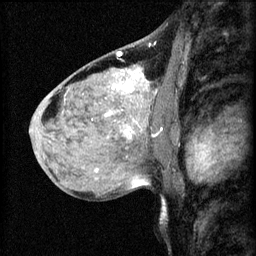
Breast MRI (dynamic contrast-enhanced), one sagittal slice; position 40 of 60 along the scan axis; 3 images stored at this slice position (order not interpretable as contrast timing); 1.5 T; TE 4.2 ms, TR 8.2 ms; 2.2 mm slice thickness; 256 × 256 image matrix. Female patient, age 40 years.
Outlined on this slice (semi-automatic segmentation, software-assisted and operator-edited):
- analysis volume of interest (the breast-tissue region the enhancement analysis was run in; not a lesion): box from (x=108, y=82) to (x=175, y=139) px
- tumour enhancement mask (voxels above the 70 % enhancement threshold inside the analysis volume of interest): (x=108, y=82)–(x=163, y=137)